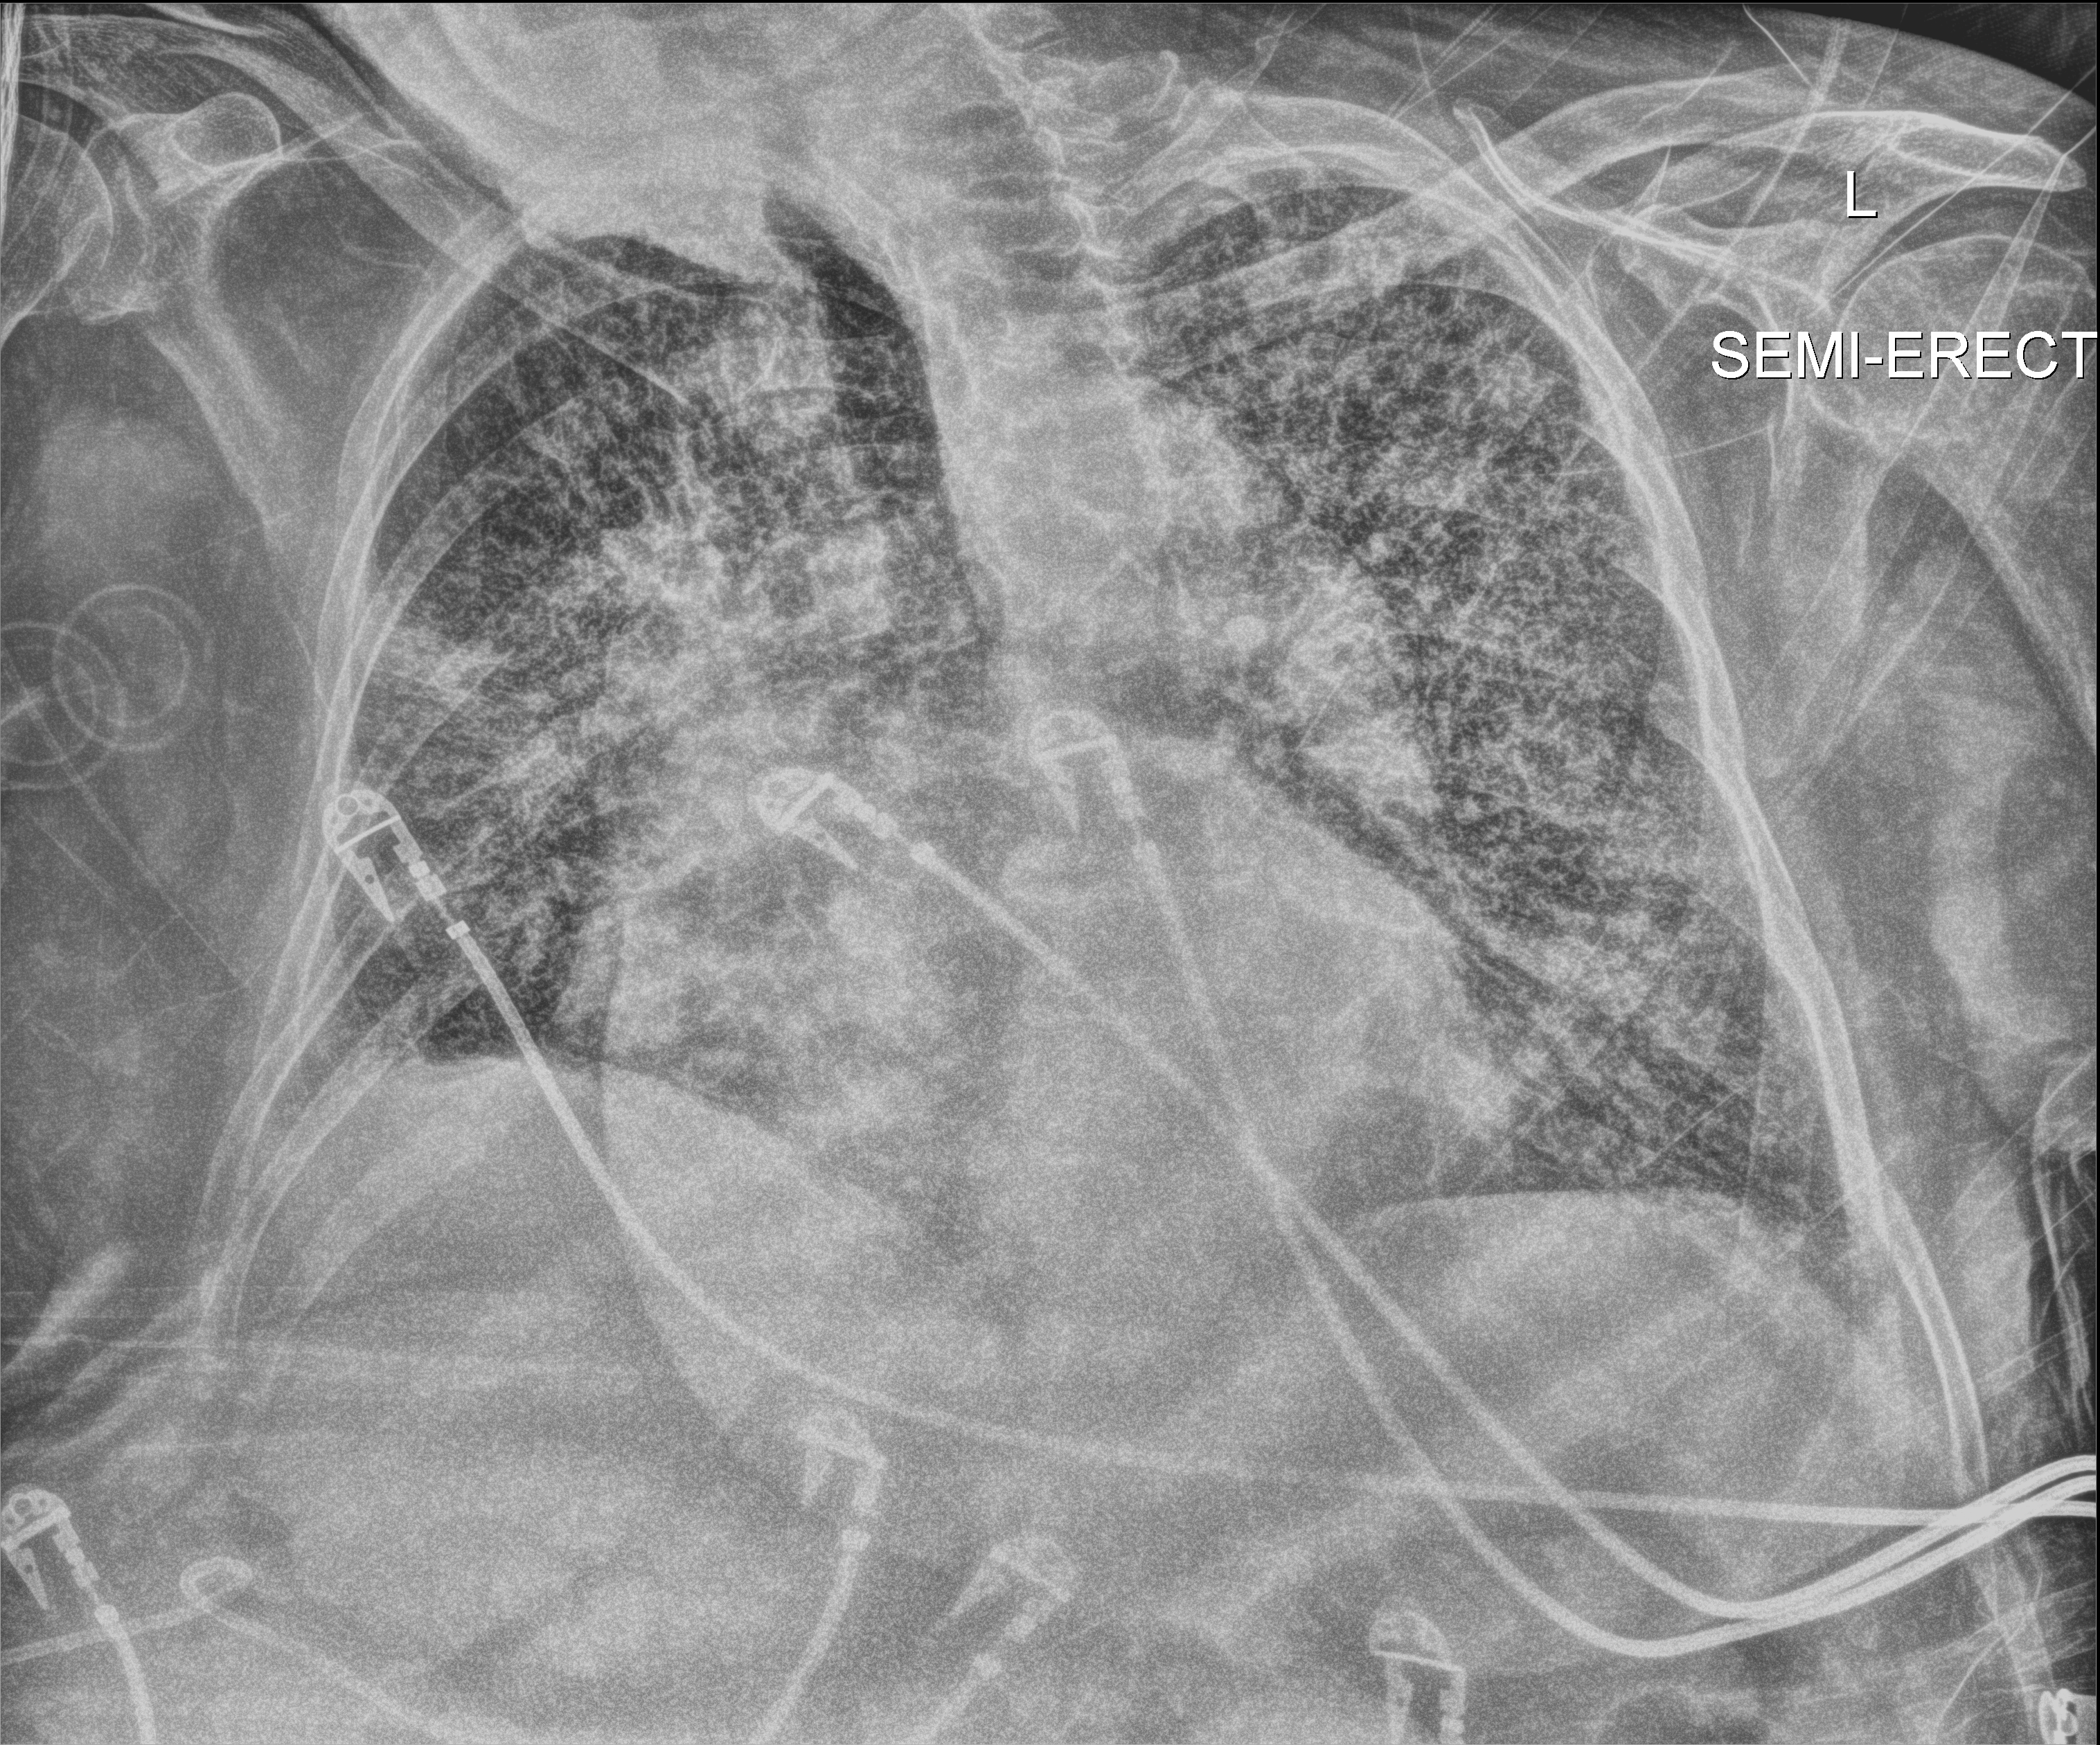
Portable chest radiograph; anteroposterior (AP) projection. Female patient hospitalised with COVID-19, age 75–90 years.
From the hospital-stay record, not from the radiograph (when in the stay this image was taken is not recorded): length of hospital stay: 17 days.